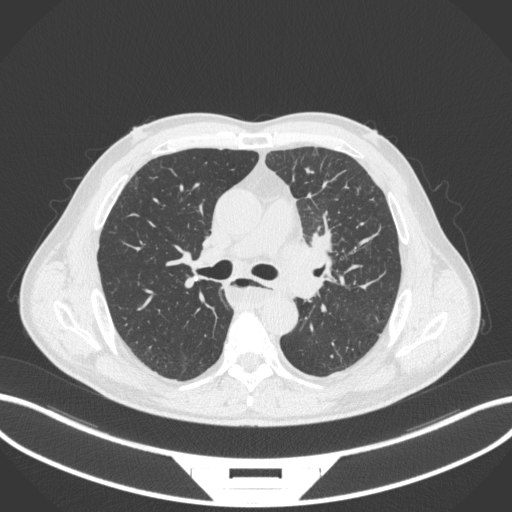
Chest CT, one axial slice; slice 233 of 411 in the series (ordered by position); reconstruction kernel B31f; 120 kVp; lung window (W 1500 / L -600 HU); 1 mm slice thickness; 512 × 512 image matrix, field of view 400 × 400 mm. Male patient, age 57 years. From the clinical record (not read from this slice): clinical TNM (as recorded): T2a N1 M0.
Structures marked on this image (rectangle marked by the reading radiologist):
- lung tumour (recorded histology: squamous cell carcinoma): bounding box [x1, y1, x2, y2] px = [275, 224, 349, 277]